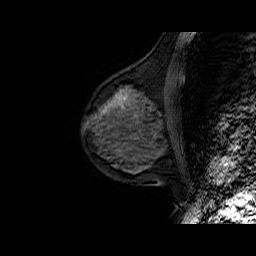
Breast MRI (dynamic contrast-enhanced), one sagittal slice; position 23 of 50 along the scan axis; dynamic contrast-enhanced series, time point 2 of 6 at this slice position (early post-contrast); 1.5 T; TE 6.5 ms, TR 32.9 ms; 4 mm slice thickness; 256 × 256 image matrix, field of view 200 × 200 mm. Female patient. Case-level facts recorded for this patient, not image findings: setting: breast cancer imaged before/during neoadjuvant chemotherapy; receptor status: HR-positive, HER2-negative.
Outlined on this slice (semi-automatic segmentation, software-assisted and operator-edited):
- analysis volume of interest (the breast-tissue region the enhancement analysis was run in; not a lesion): bounding box [x1, y1, x2, y2] px = [82, 77, 179, 149]
- tumour enhancement mask (voxels above the 100 % enhancement threshold inside the analysis volume of interest): [102, 95, 125, 113]